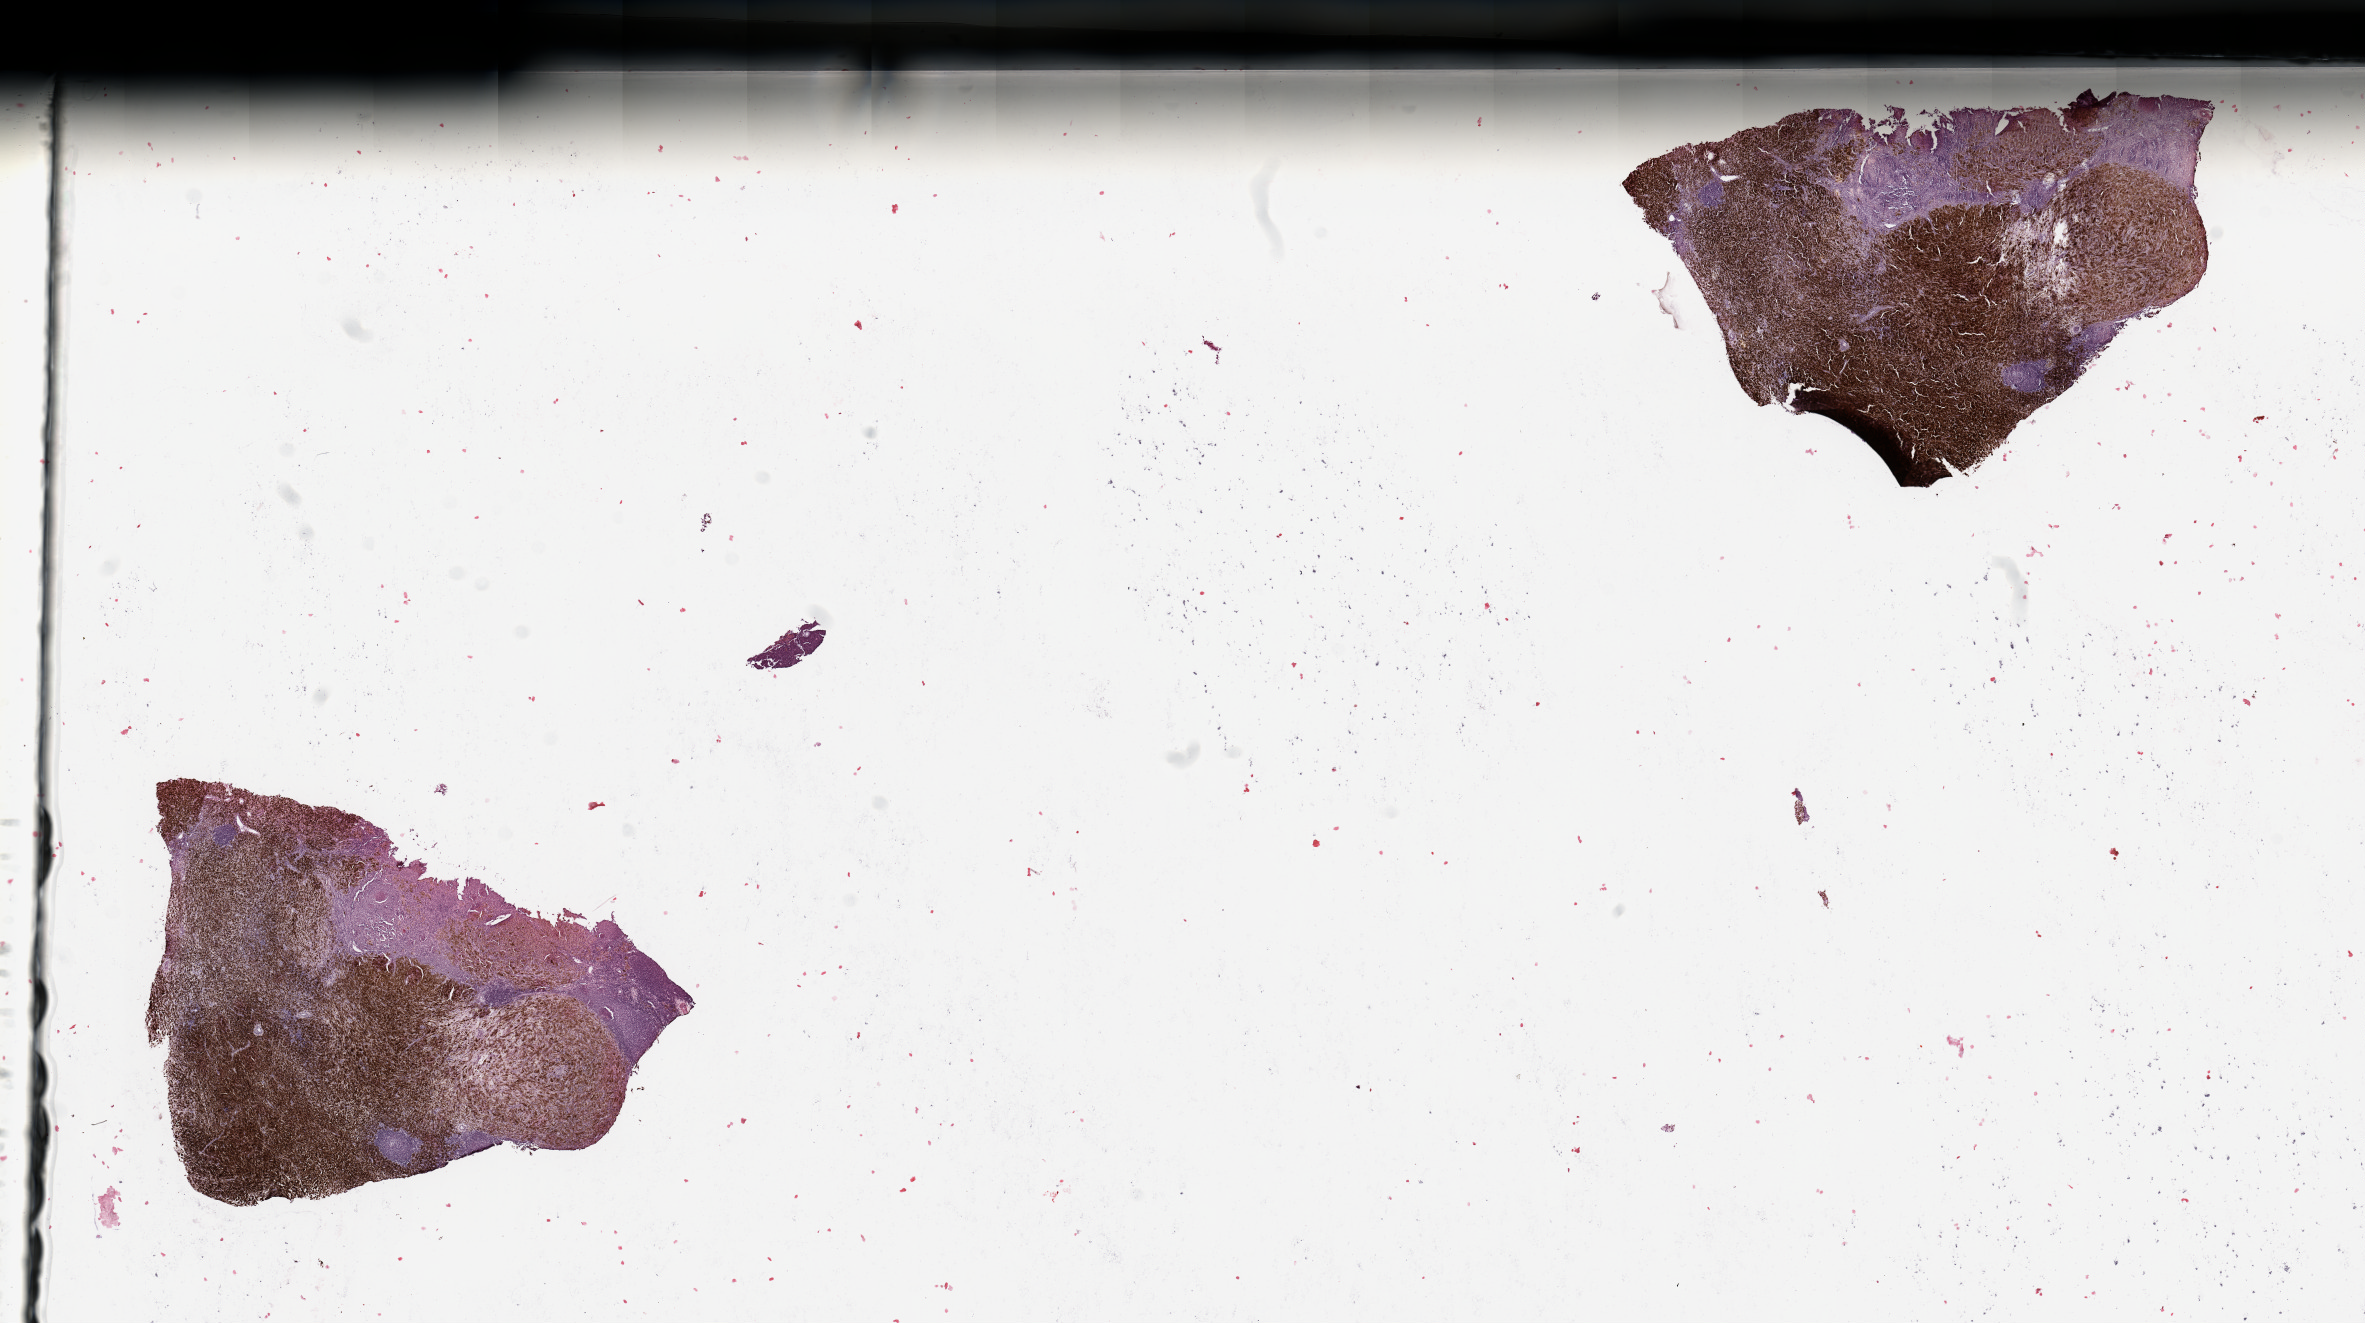
Whole-slide histology image, Hematoxylin and eosin (H&E) stained, whole scanned area (about 18.7 x 10.5 mm, slide scanned at 20x) shown as a low-resolution overview; tumour tissue sample, sampled site: lymph node. 59-year-old male patient.
- patient diagnosis (cohort enrolment): cutaneous melanoma (skin)